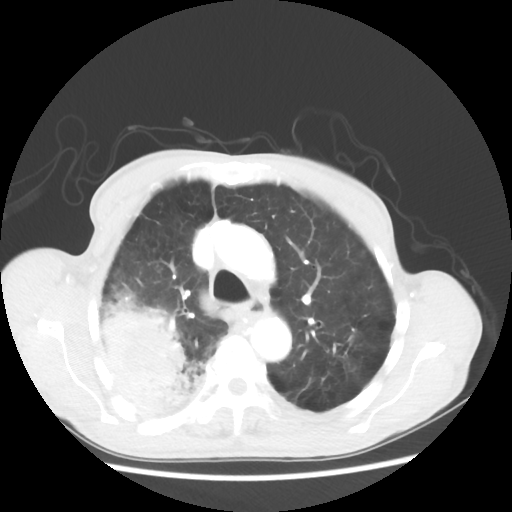
Chest CT, one axial slice. Slice 39 of 58 in the series (ordered by position). Lung window (W 1500 / L -600 HU). 5 mm slice thickness. 512 × 512 image matrix. Patient: male, 75 years. From the clinical record (not read from this slice): clinical TNM (as recorded): T4 N1 M1.
Structures marked on this image (bounding box drawn by a radiologist):
- lung tumour (recorded histology: adenocarcinoma): bounding box [x1, y1, x2, y2] px = [93, 281, 207, 419]